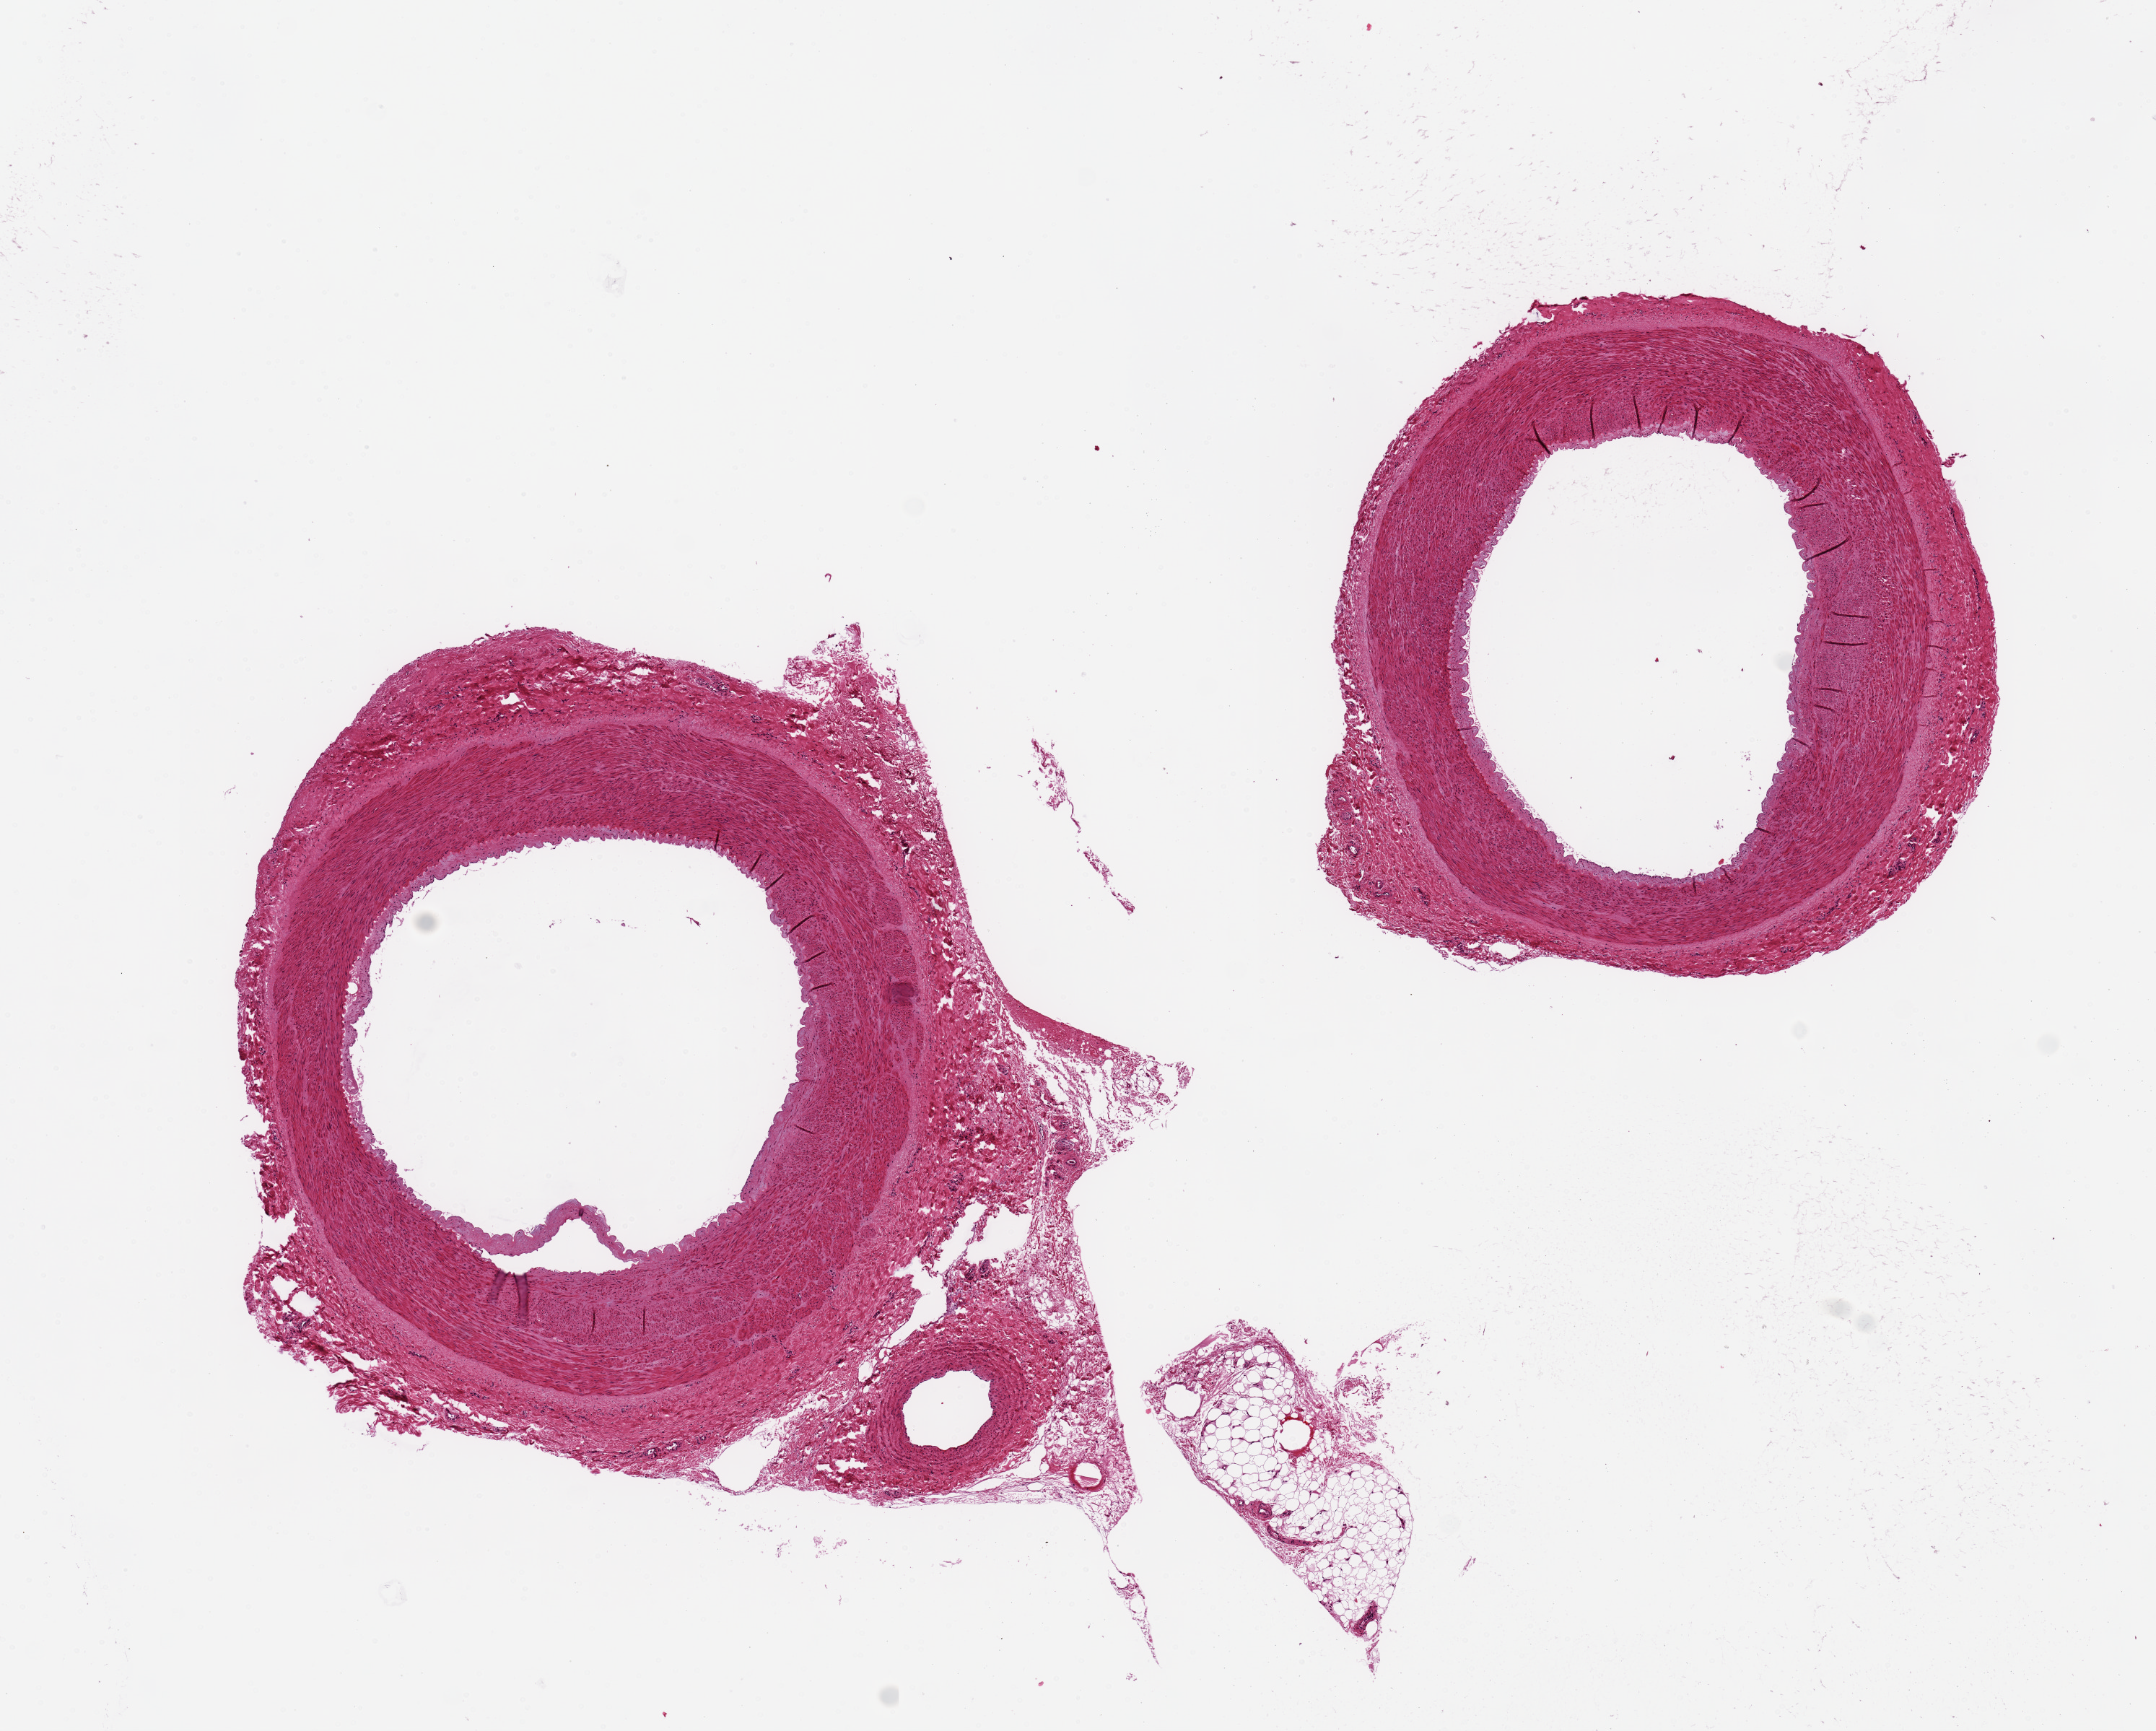
Whole-slide image, haematoxylin and eosin stain, a low-resolution overview of the entire scanned area, about 11.8 x 9.5 mm (slide scanned at 20x); PAXgene-fixed paraffin-embedded (PFPE) section; sampled site (target tissue): tibial artery; tissue donor sample. Donor: male.
* reviewer comment on this tissue sample: 2 pieces; no lesions